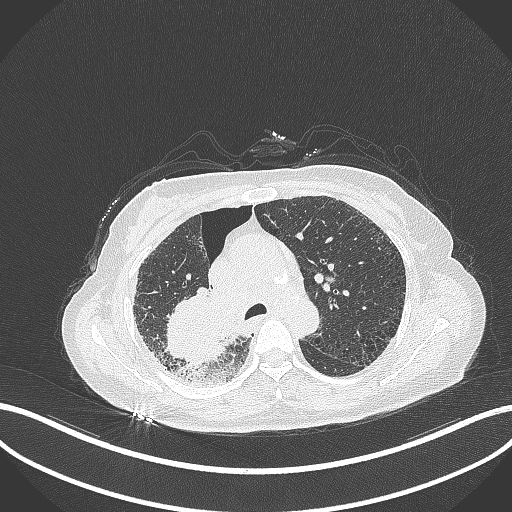
Chest CT, one axial slice. Position 232 of 408 along the scan axis. Reconstruction kernel B70f. 120 kVp. Lung window (W 1500 / L -600 HU). 1 mm slice thickness. 512 × 512 image matrix. Patient: female, 64 years. Case-level facts recorded for this patient, not image findings: clinical TNM (as recorded): T3 N3 M0.
Structures marked on this image (rectangle marked by the reading radiologist):
- lung tumour (recorded histology: squamous cell carcinoma): bounding box (x1, y1, x2, y2) in pixels: (158, 286, 236, 375)